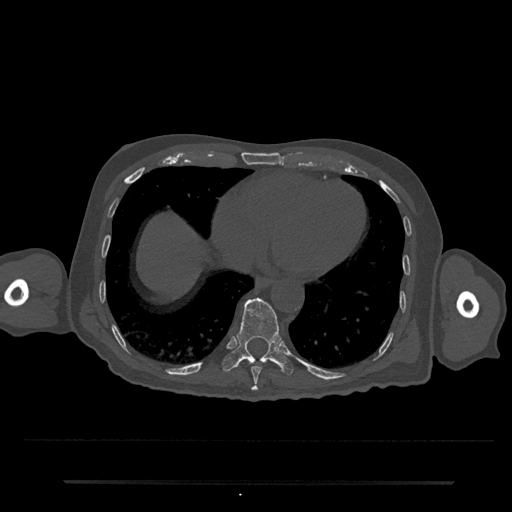
CT including the spine, one axial slice; slice 328 of 797 in the series (ordered by position); bone window (W 1800 / L 400 HU); 512 × 512 image matrix. Patient: male, 74 years. From the clinical record (not read from this slice): primary cancer: prostate.
Annotated regions visible in this slice (semi-automatic segmentation, software-assisted and operator-edited):
- T10 vertebra: bounding box [x1, y1, x2, y2] px = [222, 298, 293, 375]
- T9 vertebra: [251, 362, 262, 391]